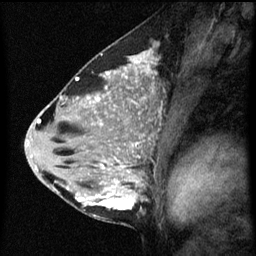
Breast MRI (dynamic contrast-enhanced), one sagittal slice. Slice 31 of 60 in the series (ordered by position). Dynamic contrast-enhanced series, image 2 of 3 at this slice position (ordered by acquisition). 1.5 T. TE 4.2 ms, TR 8 ms. 256 × 256 image matrix. Female patient, age 33 years.
Outlined on this slice (semi-automatically segmented with operator editing):
- analysis volume of interest (the breast-tissue region the enhancement analysis was run in; not a lesion): bounding box [x1, y1, x2, y2] px = [71, 118, 160, 217]
- tumour enhancement mask (voxels above the 70 % enhancement threshold inside the analysis volume of interest): [76, 142, 138, 211]